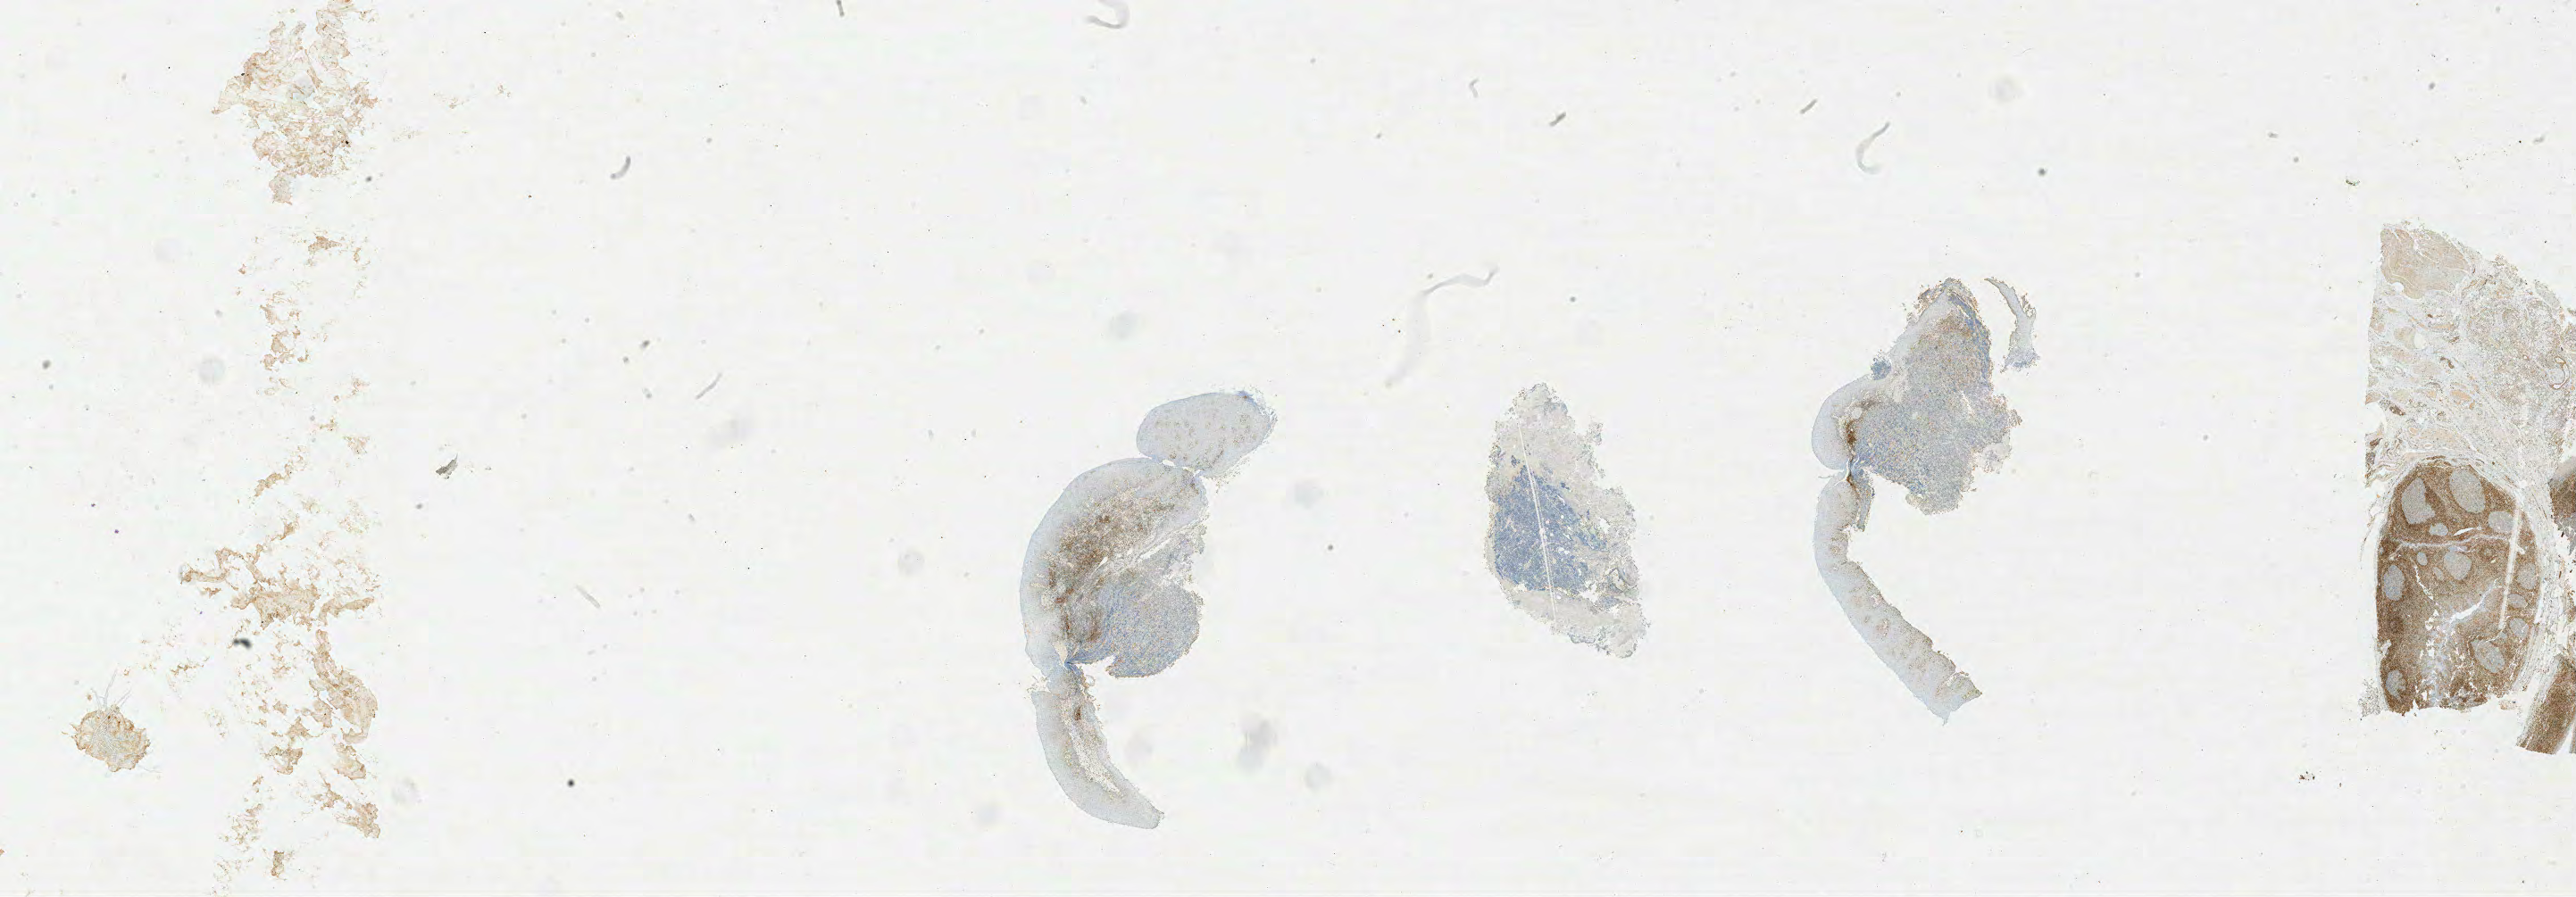
Immunohistochemistry (IHC) whole-slide image stained for BCL2, low-resolution overview of the scanned area, about 46.0 x 16.0 mm, tumor tissue. Patient: male, 66 years old.
- diagnosis: Burkitt lymphoma, NOS